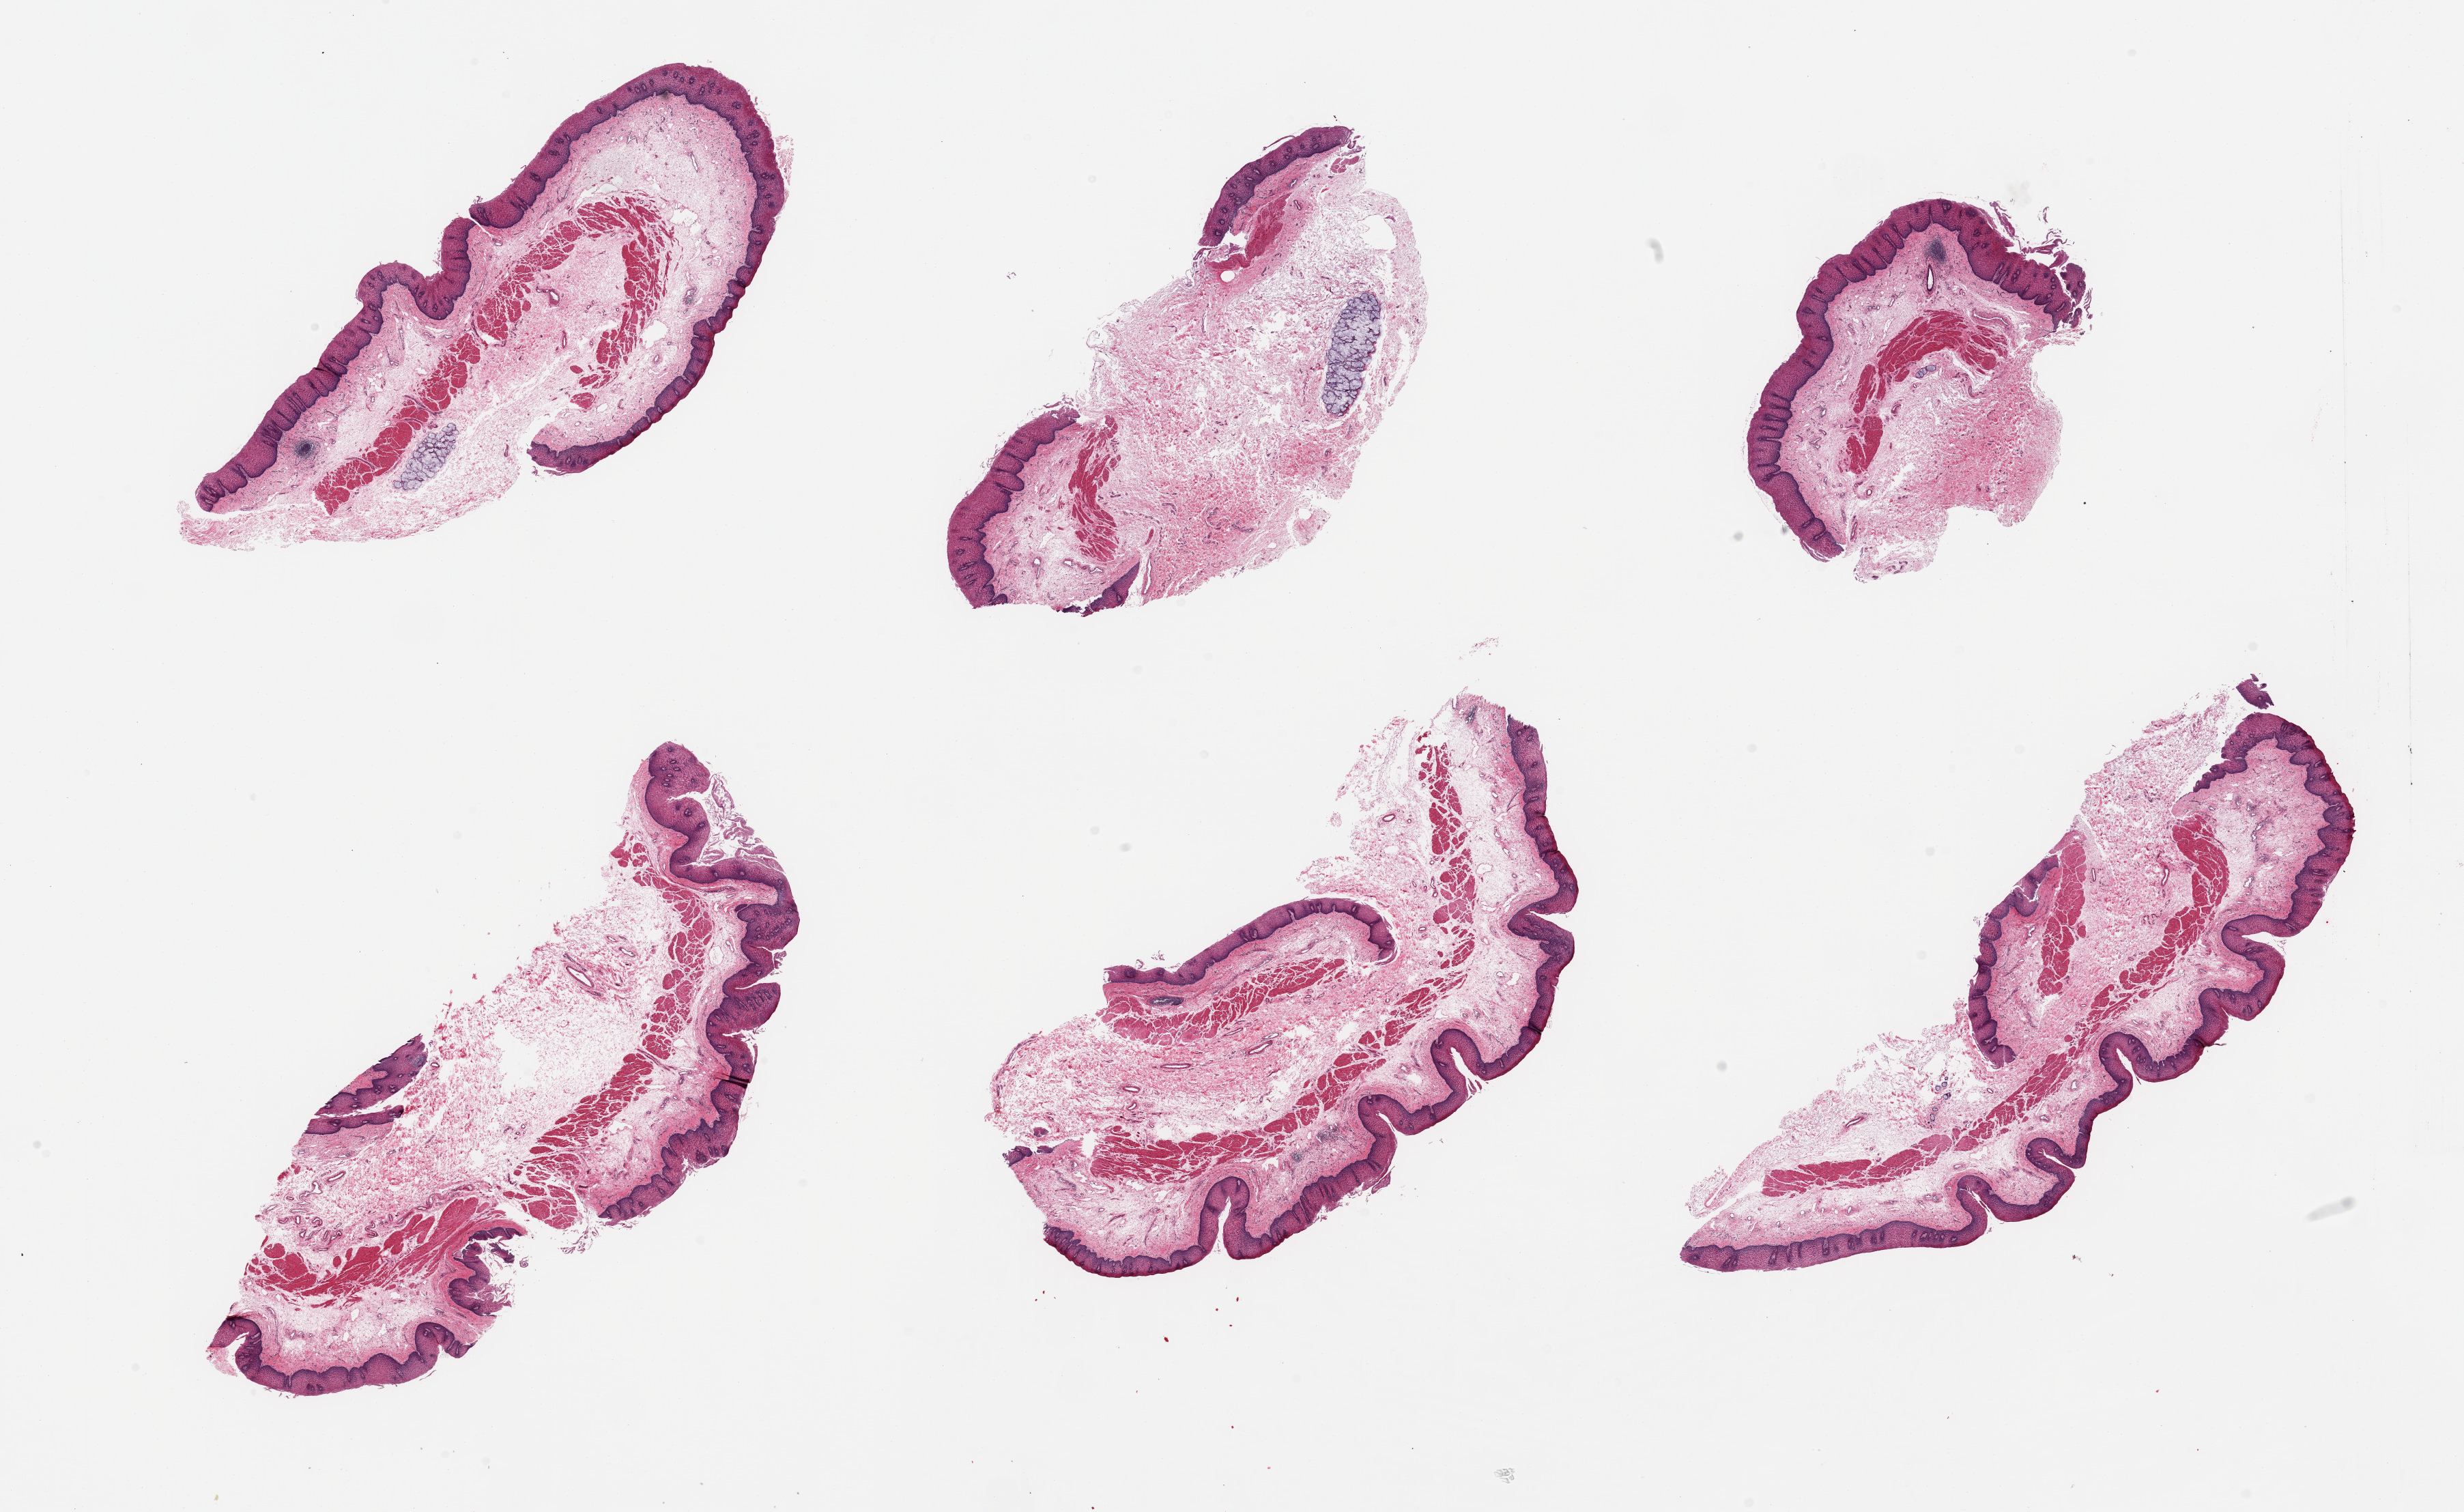
Whole-slide image, H&E stain, low-resolution overview of the scanned area, about 28.5 x 17.5 mm (slide scanned at 20x); PAXgene-fixed paraffin-embedded (PFPE) section; section of esophageal mucous membrane (target tissue); donor tissue sample. Donor sex: female.
Review note (as recorded): 6 pieces; edematous lamina propria and submucosa.